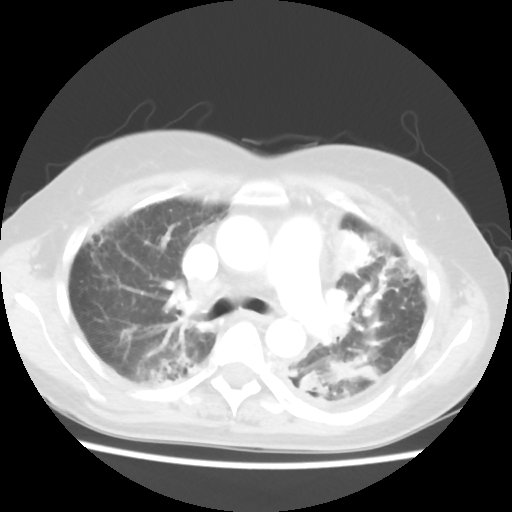
Chest CT, one axial slice. Position 38 of 56 along the scan axis. 120 kVp. Lung window (W 1500 / L -600 HU). 5 mm slice thickness. 512 × 512 image matrix, field of view 309 × 309 mm. Patient: female, 56 years. From the clinical record (not read from this slice): clinical TNM (as recorded): T1c N0 M1.
Structures marked on this image (rectangle marked by the reading radiologist):
- lung tumour (recorded histology: adenocarcinoma): bounding box [x1, y1, x2, y2] px = [319, 215, 374, 284]